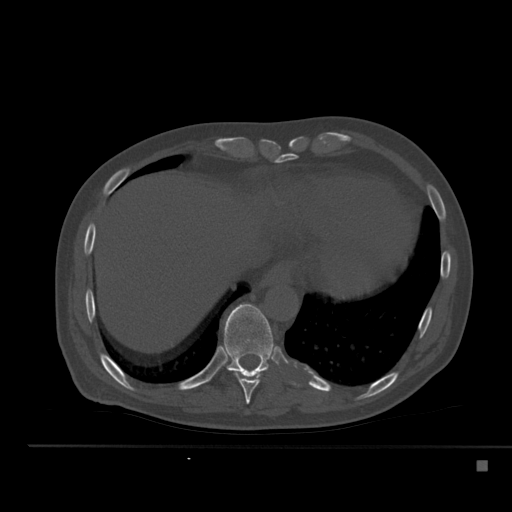
CT including the spine, one axial slice. Slice 277 of 517 in the series (ordered by position). 120 kVp. Bone window (W 1800 / L 400 HU). 1.5 mm slice thickness. 512 × 512 image matrix, field of view 408 × 408 mm. Male patient, age 70 years. Case-level facts recorded for this patient, not image findings: primary cancer: renal; vertebrae with lytic lesions (as recorded): T4, T6, T10, T12, L3, L4, L5.
Structures marked on this image (semi-automatic segmentation, software-assisted and operator-edited):
- T10 vertebra: bounding box <224,303,277,377> (left, top, right, bottom; pixels)
- T9 vertebra: <232,370,263,404>